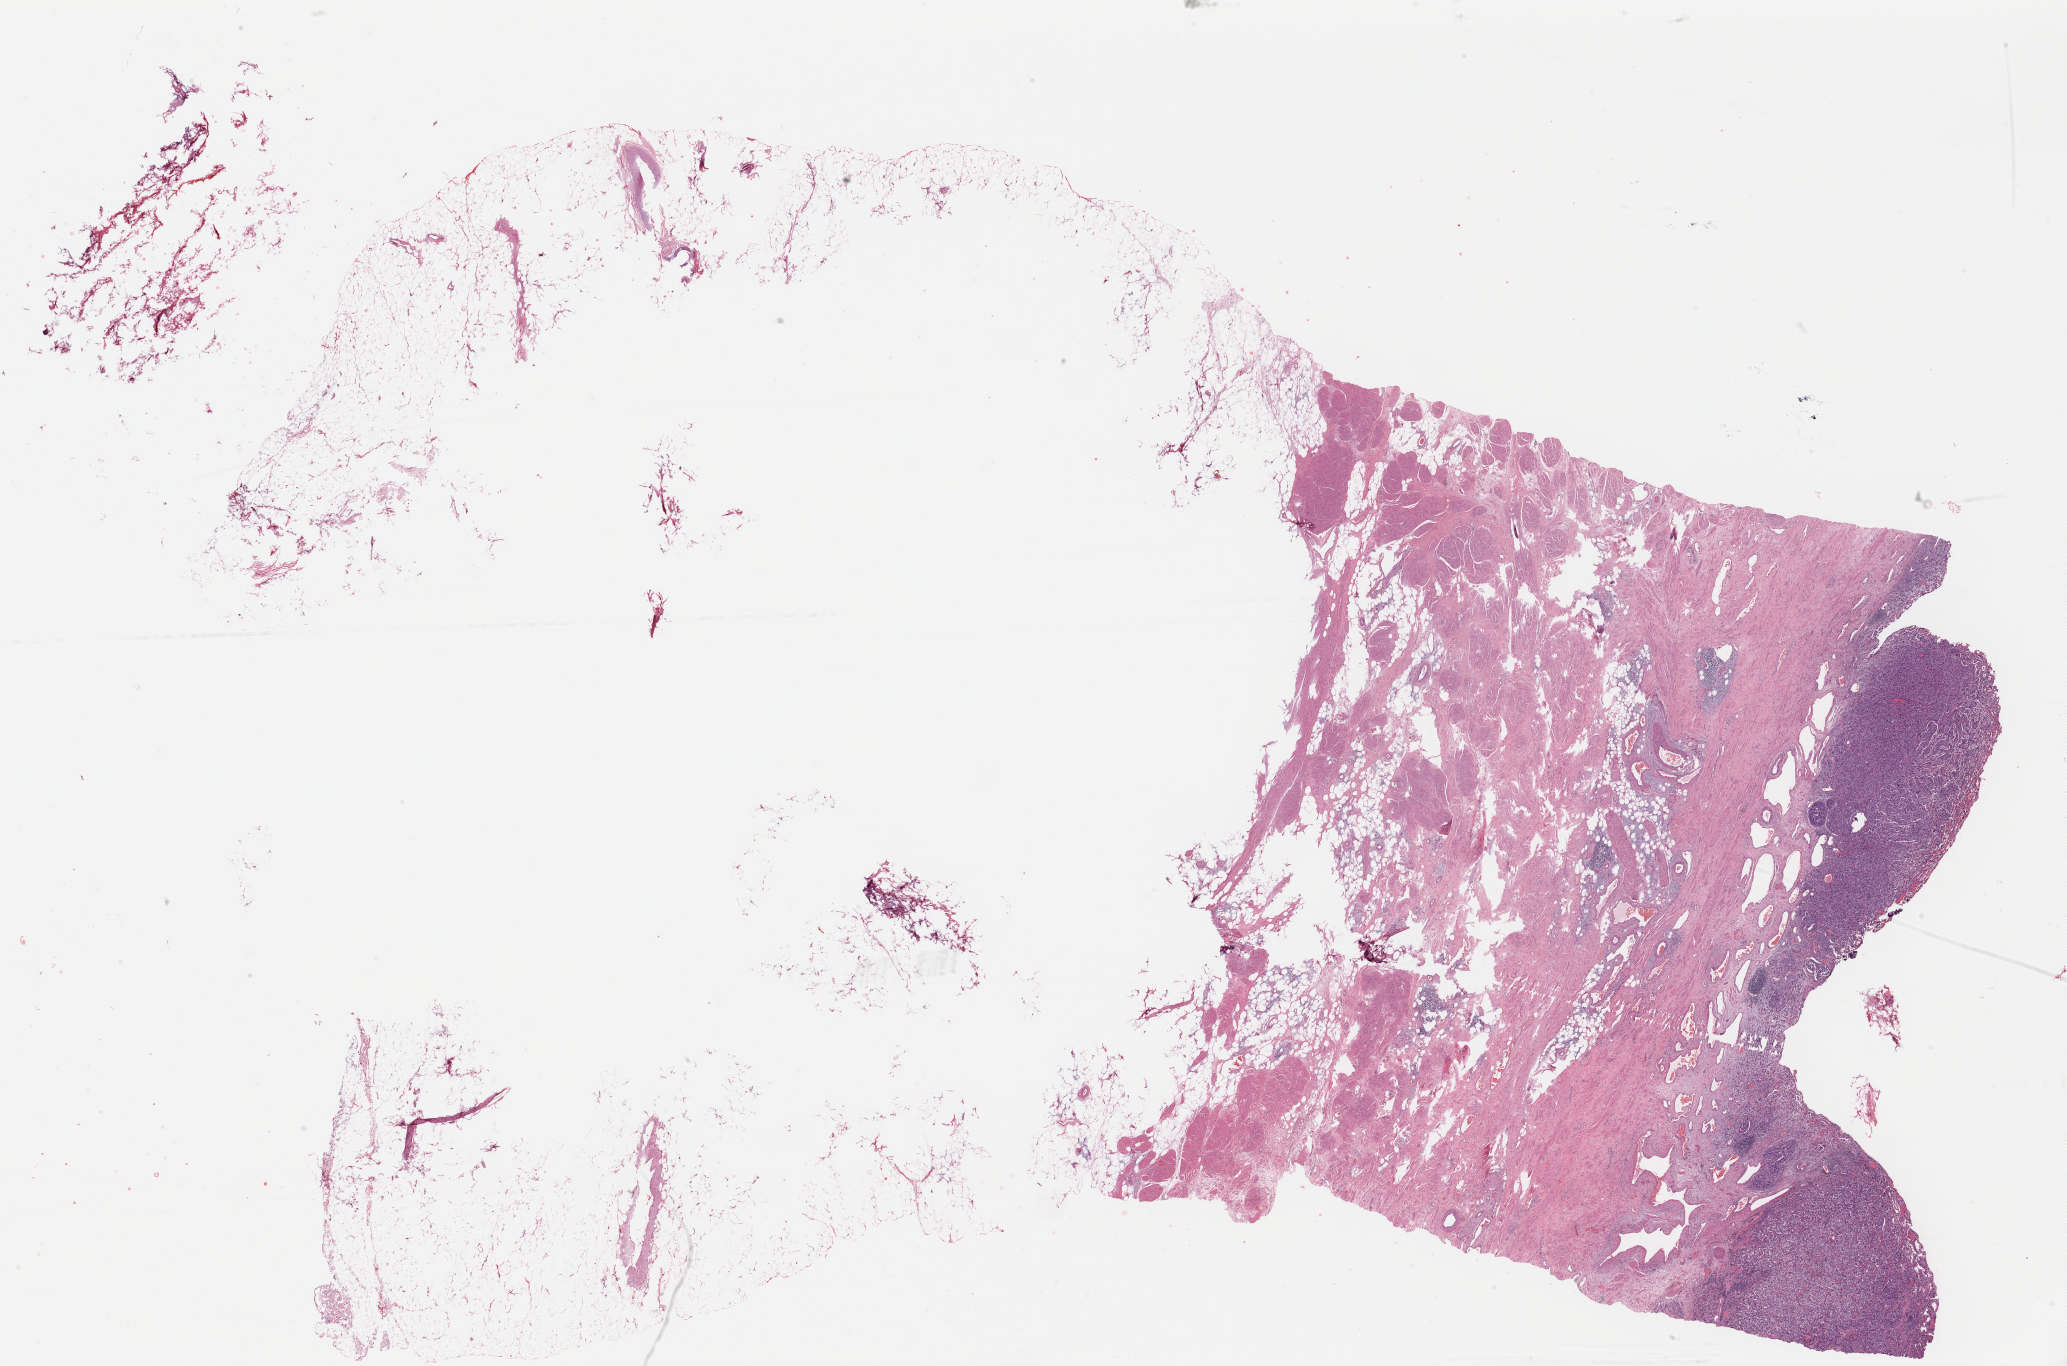
H&E-stained whole-slide image — whole scanned area (about 32.5 x 21.5 mm) shown as a low-resolution overview, formalin-fixed paraffin-embedded (FFPE) diagnostic section, bladder, primary tumour sample. Male, age 76 years at initial diagnosis. Histologic grade: high grade.
Pathologic diagnosis: Transitional cell carcinoma. AJCC pathologic stage: IV. Lymph nodes positive (case pathology): 2 of 47 examined.